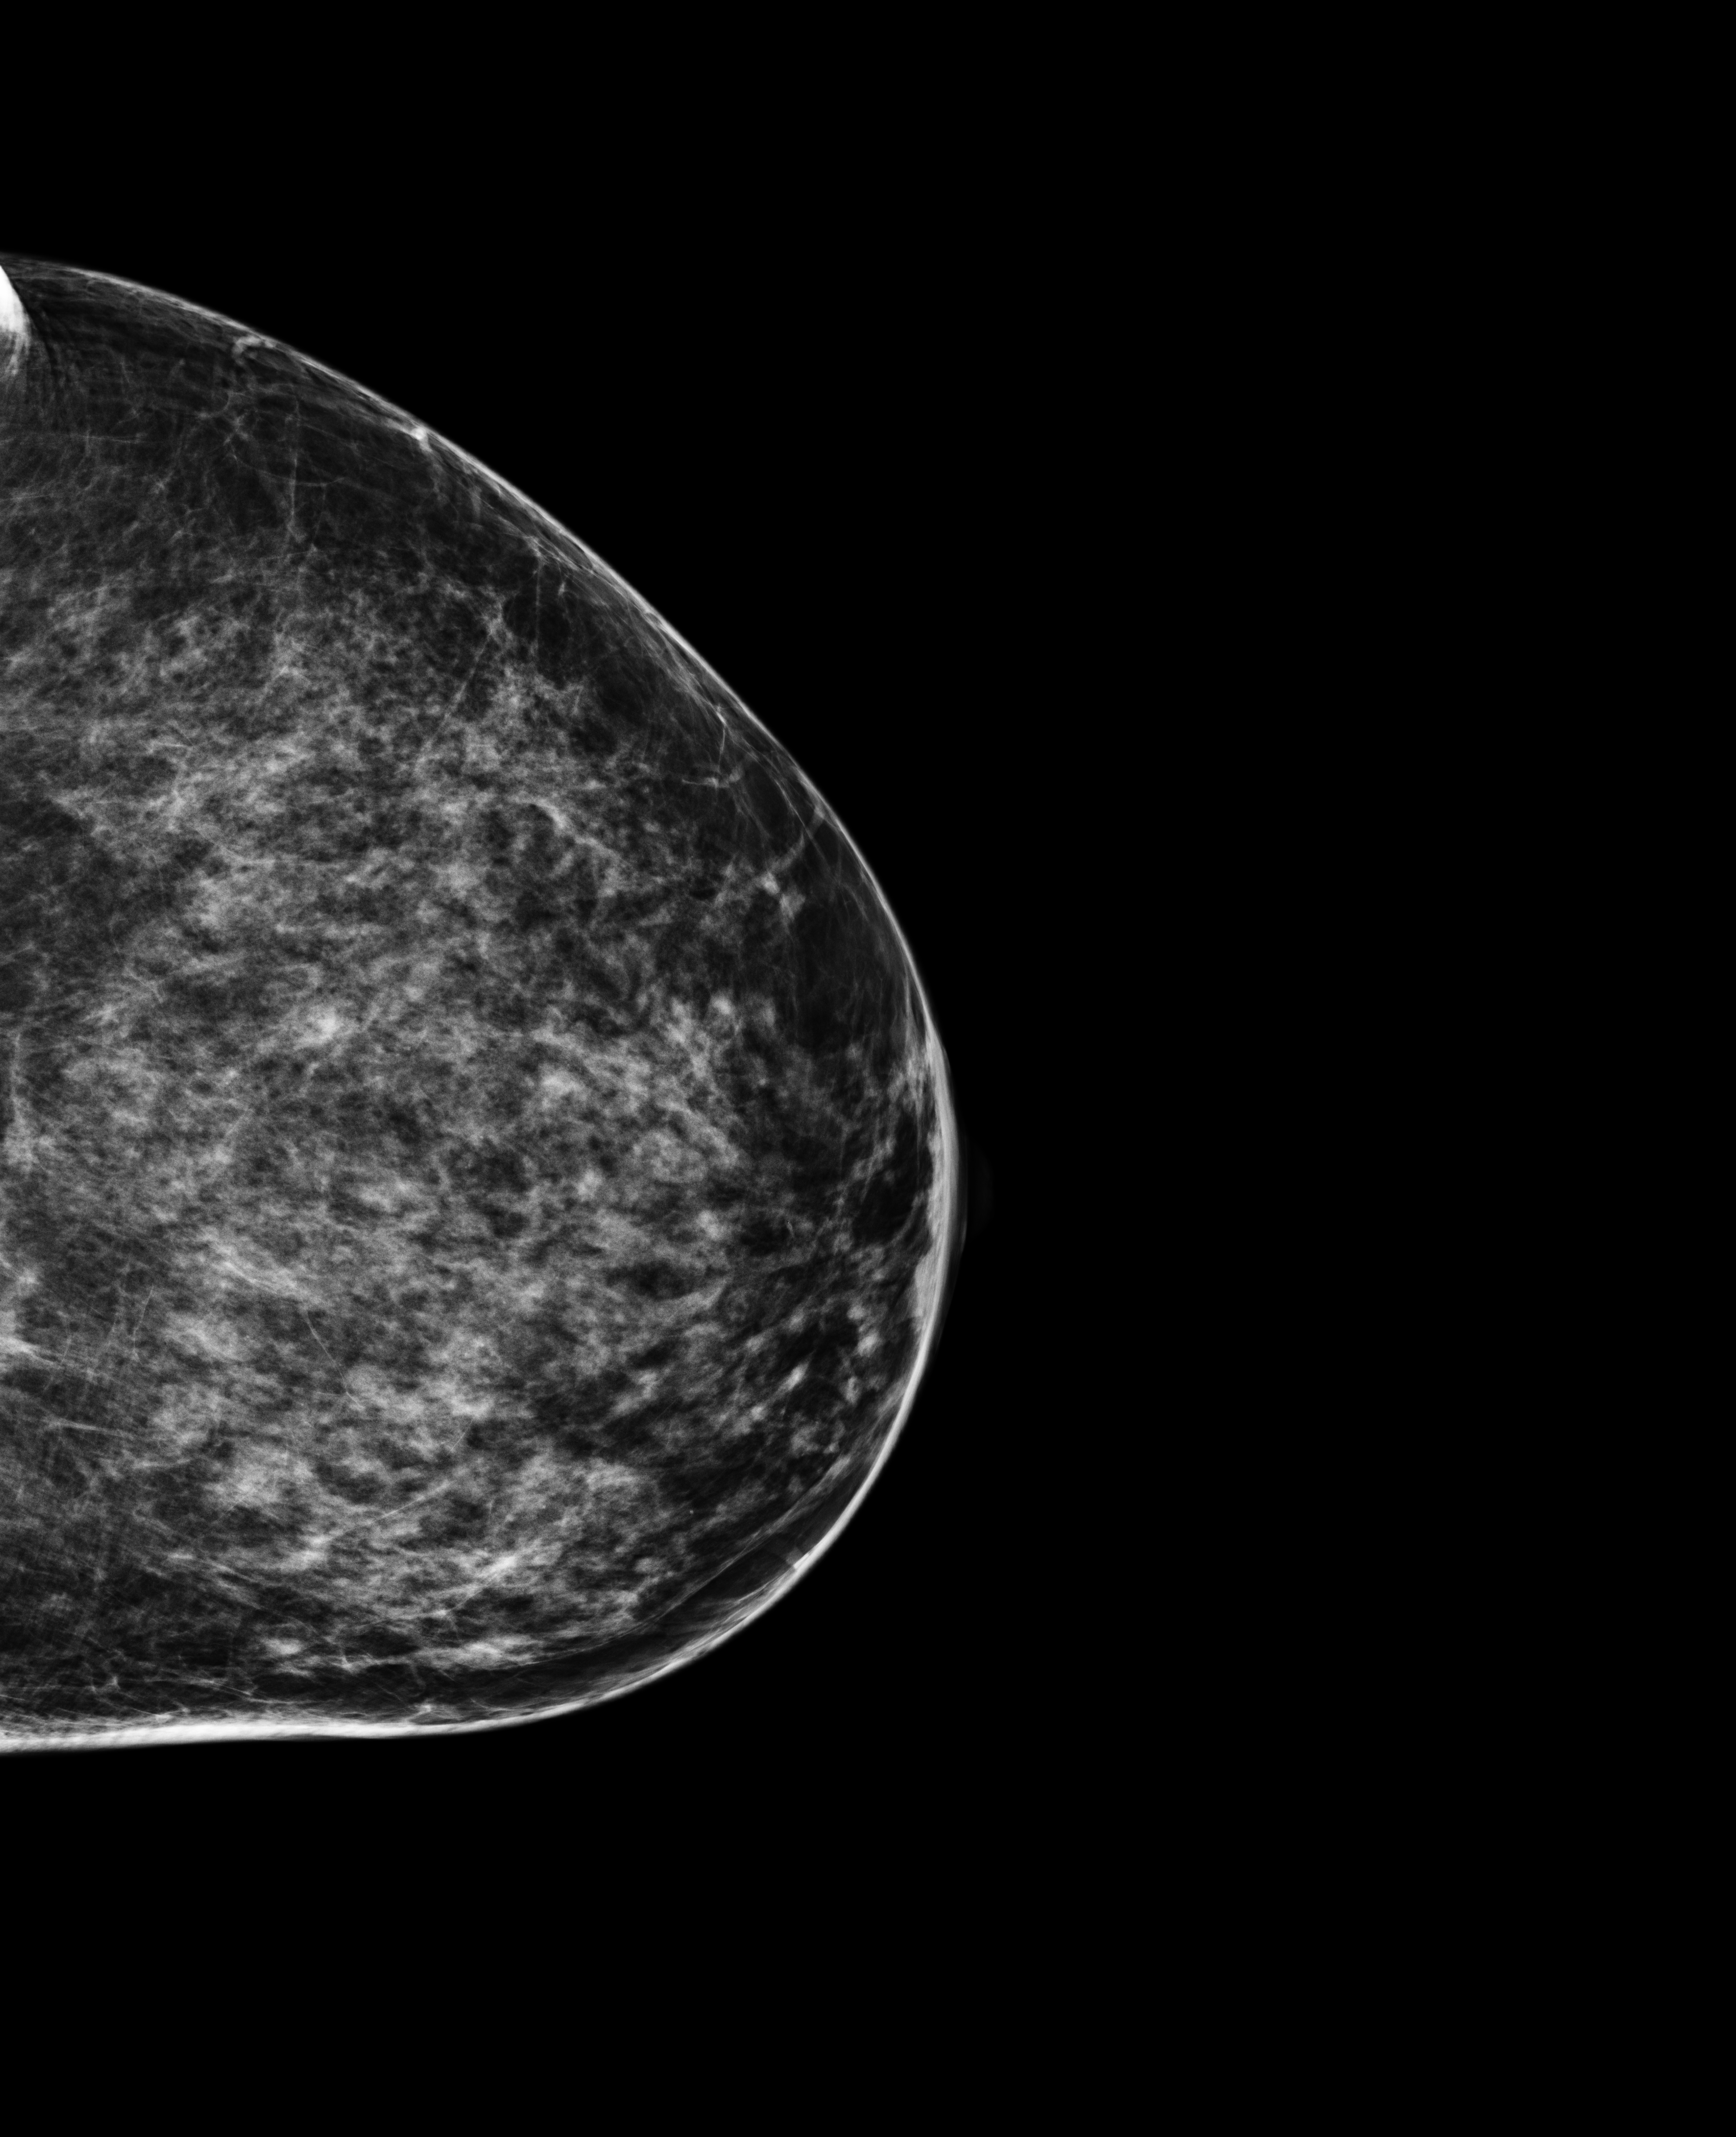
Digital mammogram (FFDM); left breast; cranio-caudal projection; annual screening mammography examination; compressed breast thickness 76 mm. Patient: female, 50 years.
Breast density at the screening exam (both breasts): heterogeneously dense (BI-RADS density category c).